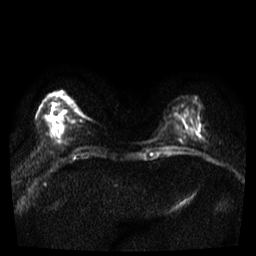
Breast MRI, one axial slice; position 9 of 36 along the scan axis; diffusion-weighted series; image 2 of 4 stored at this slice position (different b-values; order by instance number); 3 T; 256 × 256 image matrix, field of view 300 × 300 mm. Female patient.
Annotated regions visible in this slice (expert manual segmentation):
- tumour on diffusion-weighted imaging: bounding box [x1, y1, x2, y2] px = [55, 117, 65, 132]